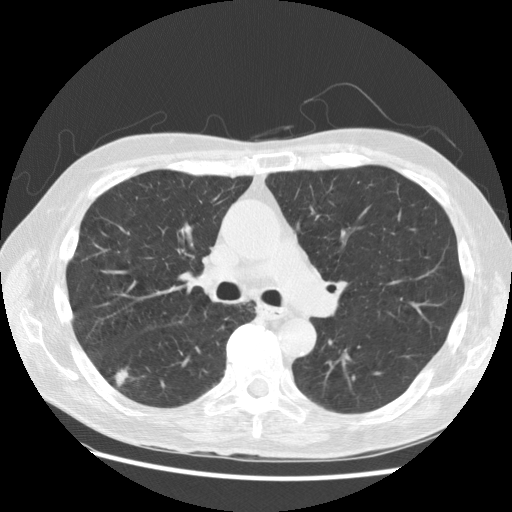
Low-dose screening chest CT, one axial slice; reconstruction kernel STANDARD; 120 kVp; lung window (W 1500 / L -600 HU); 2.5 mm slice thickness; 512 × 512 image matrix.
Annotated regions visible in this slice (manually delineated by an expert):
- lesion 1 (tumor, lower lobe of right lung): bounding box (x1, y1, x2, y2) in pixels: (116, 370, 129, 386)